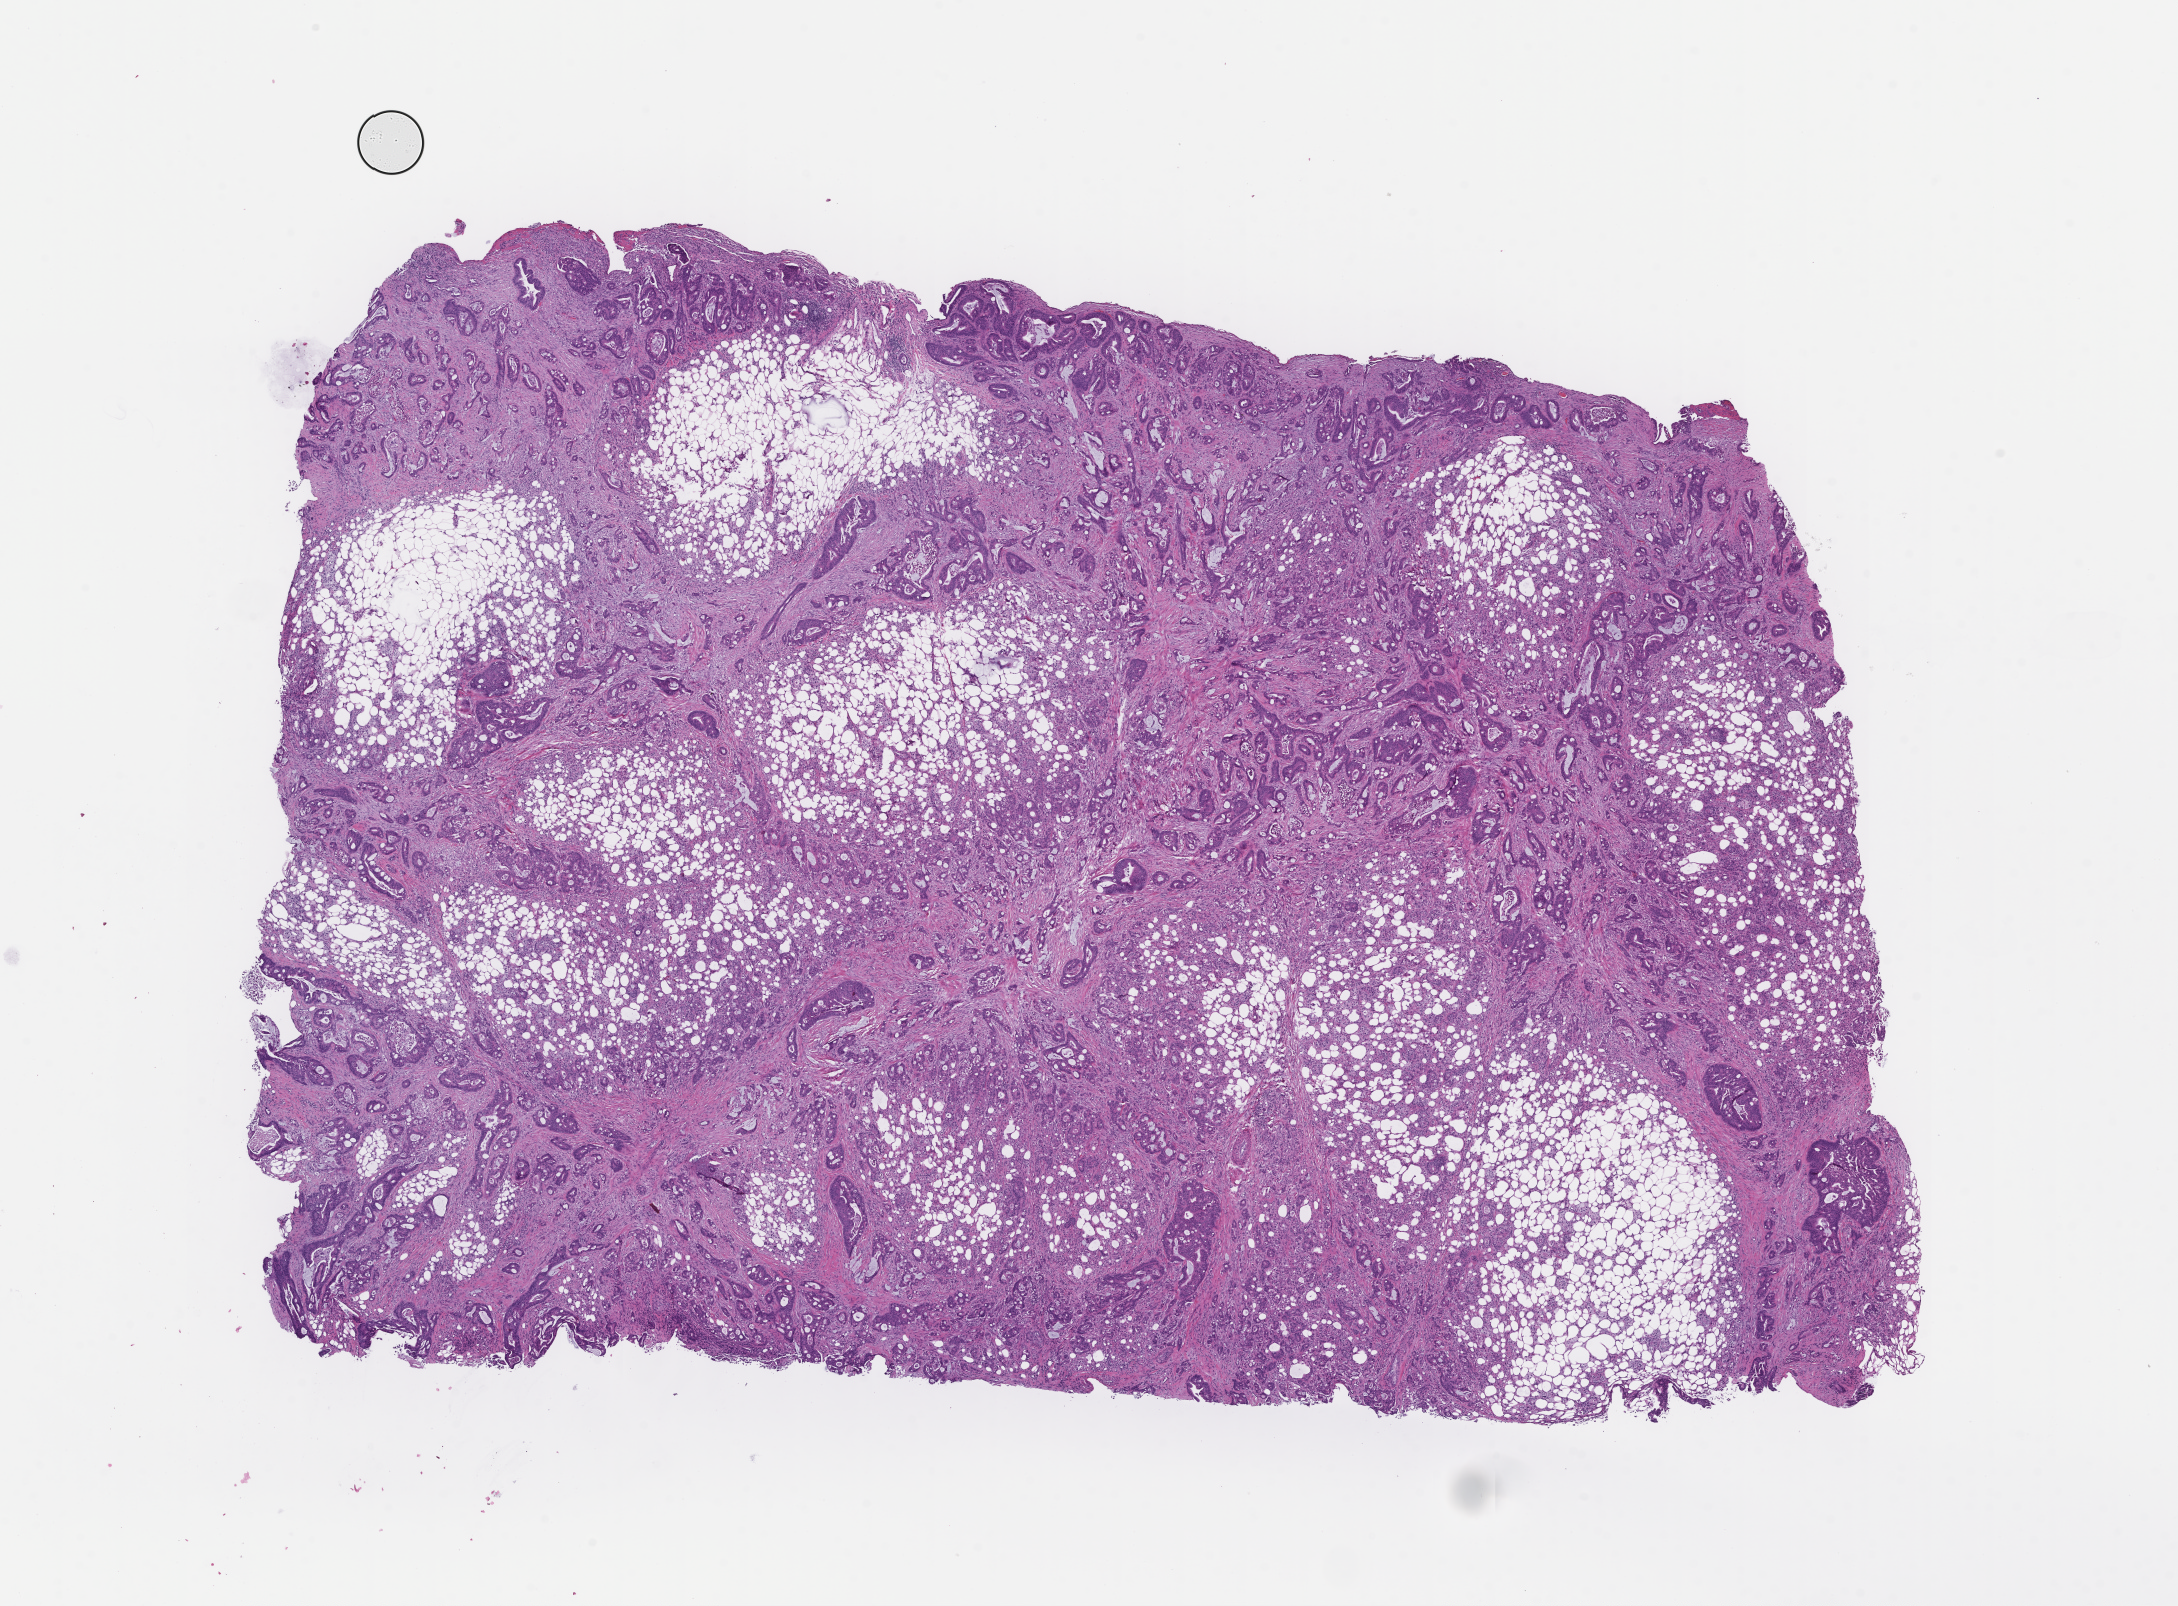
H&E whole-slide image, whole scanned area (about 17.6 x 13.0 mm) shown as a low-resolution overview, formalin-fixed paraffin-embedded section, specimen time point: collected at baseline (before treatment). Female patient.
• this section: metastatic tumor tissue
• patient diagnosis (primary): Colorectal Carcinoma